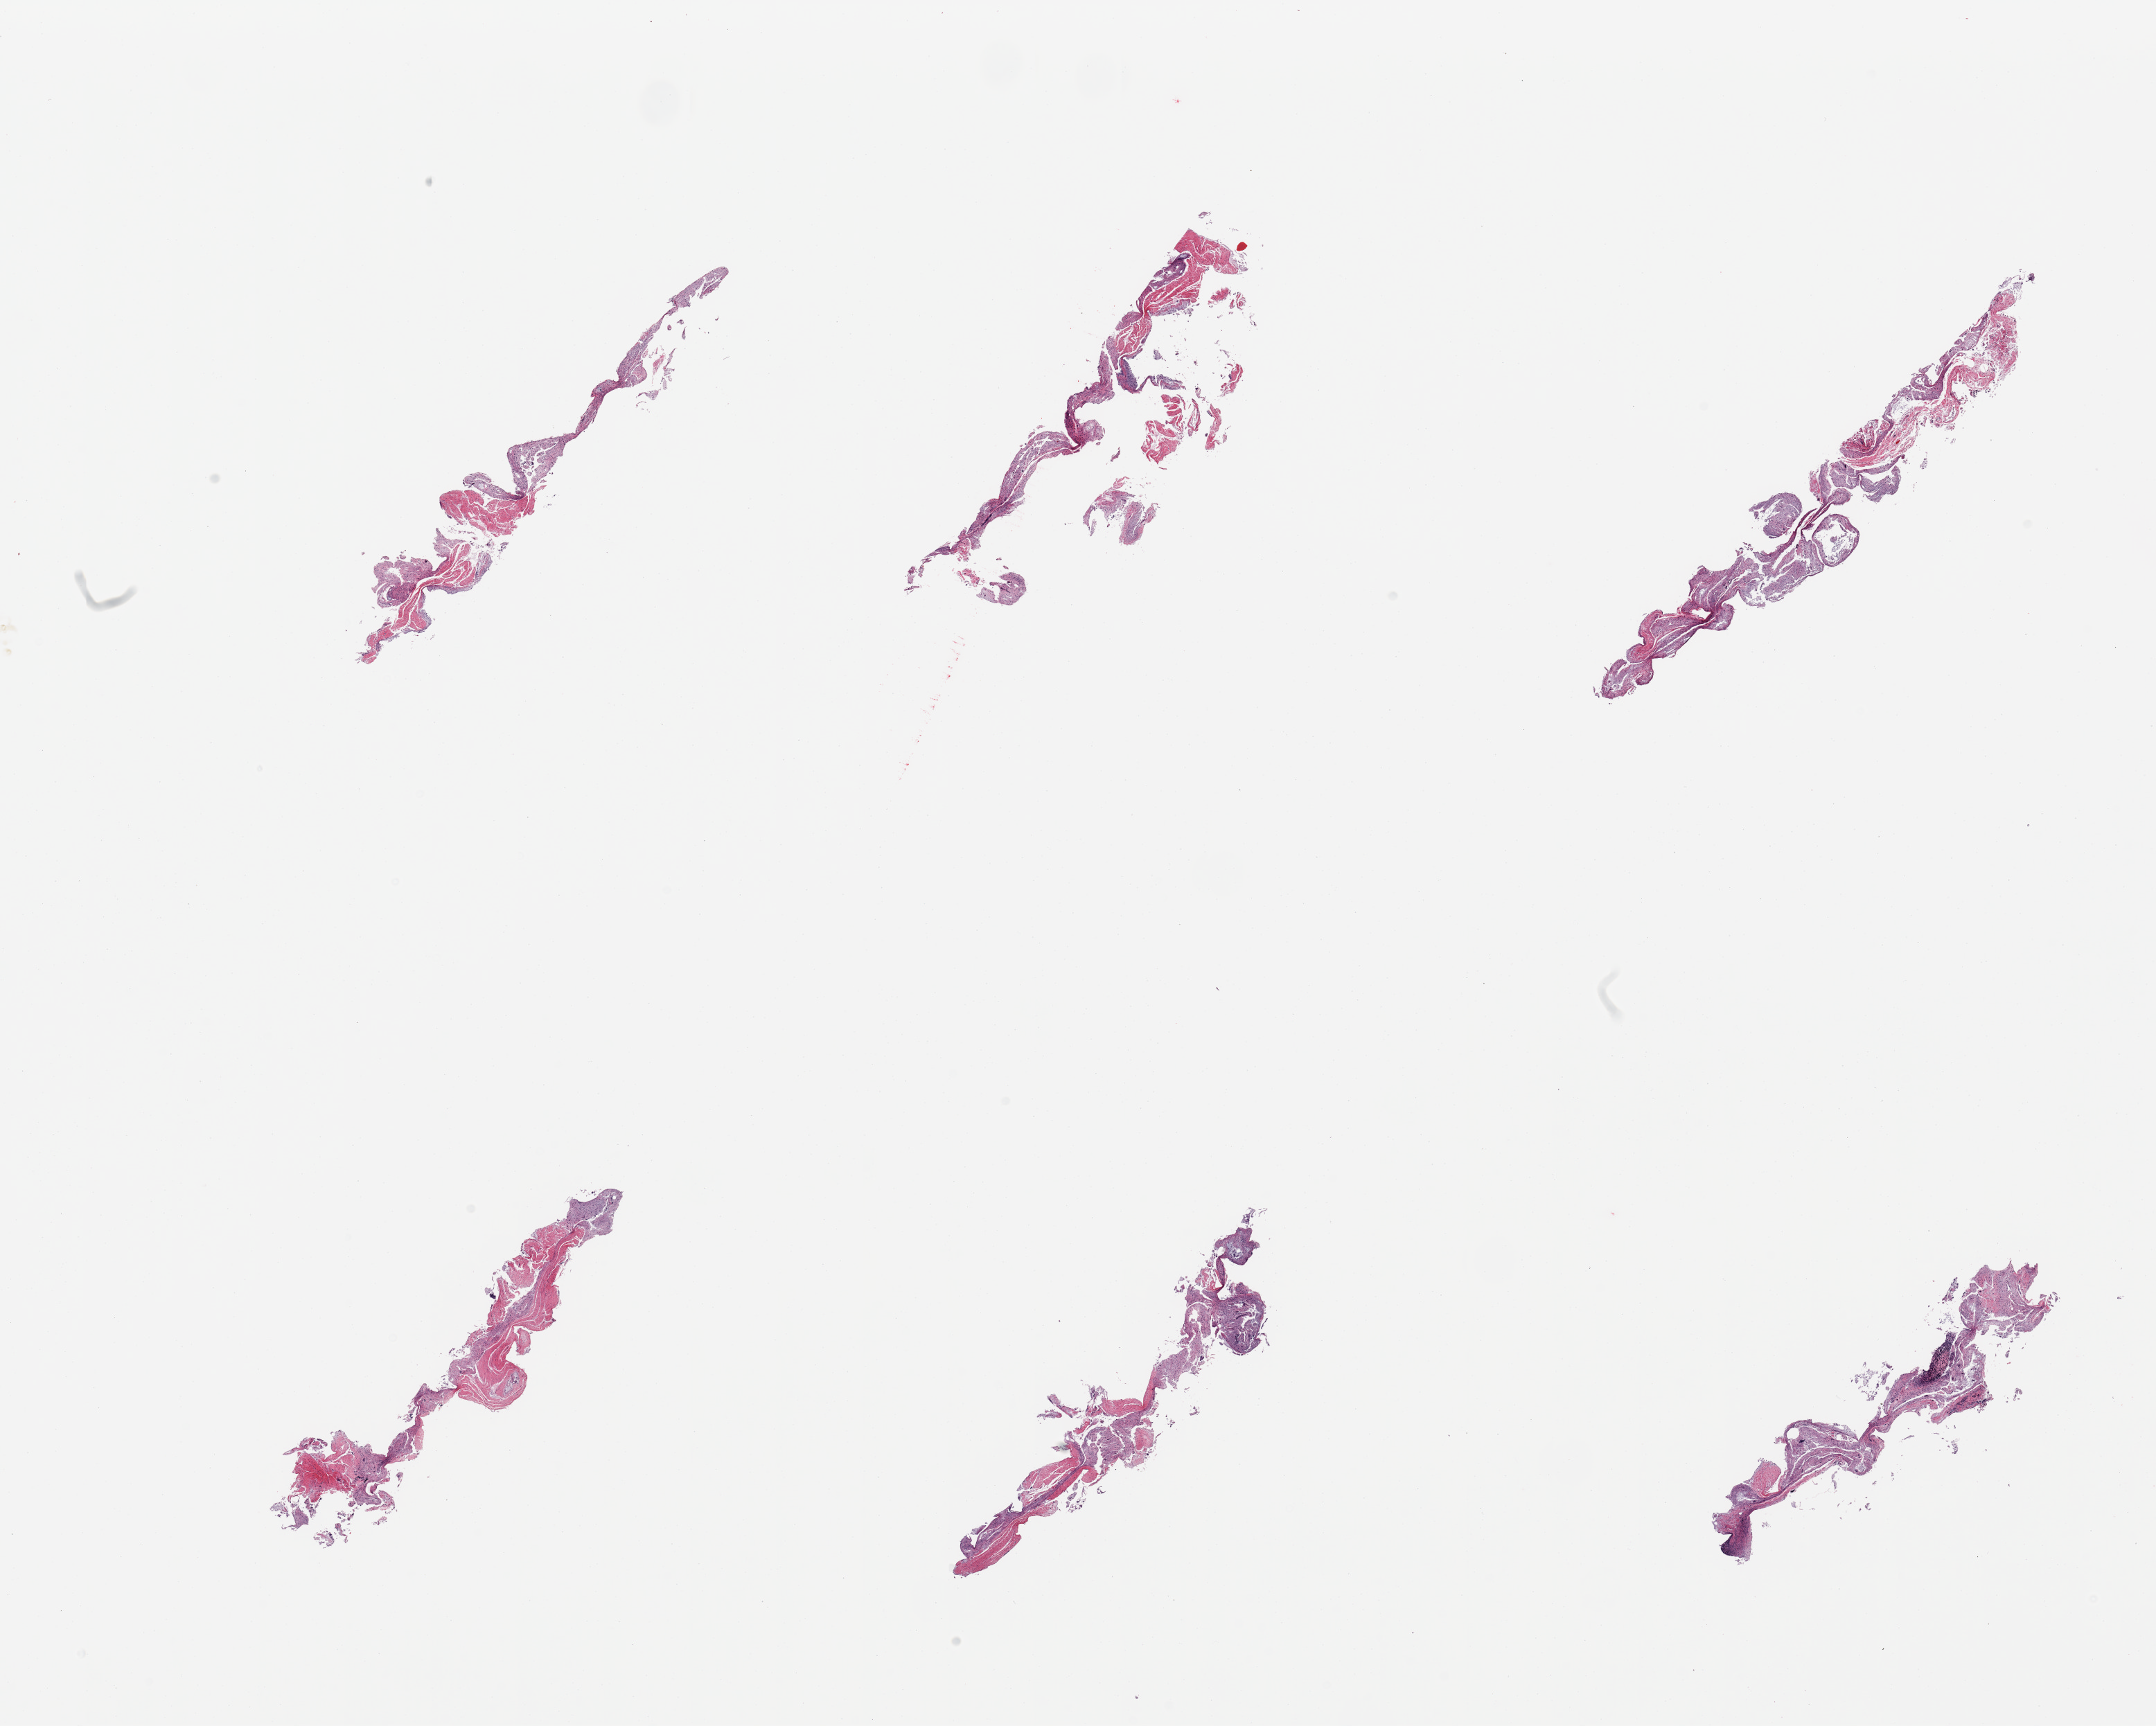
Digitized haematoxylin and eosin-stained section — shown as a low-resolution overview of the whole scanned area (about 24.6 x 19.7 mm), PAXgene-fixed paraffin-embedded (PFPE) section, section of ileum (target tissue), tissue donor sample.
Reviewer comment on this tissue sample: 6 pieces; virtually no lymphoid tissue in strips of autolyzed mucosa.